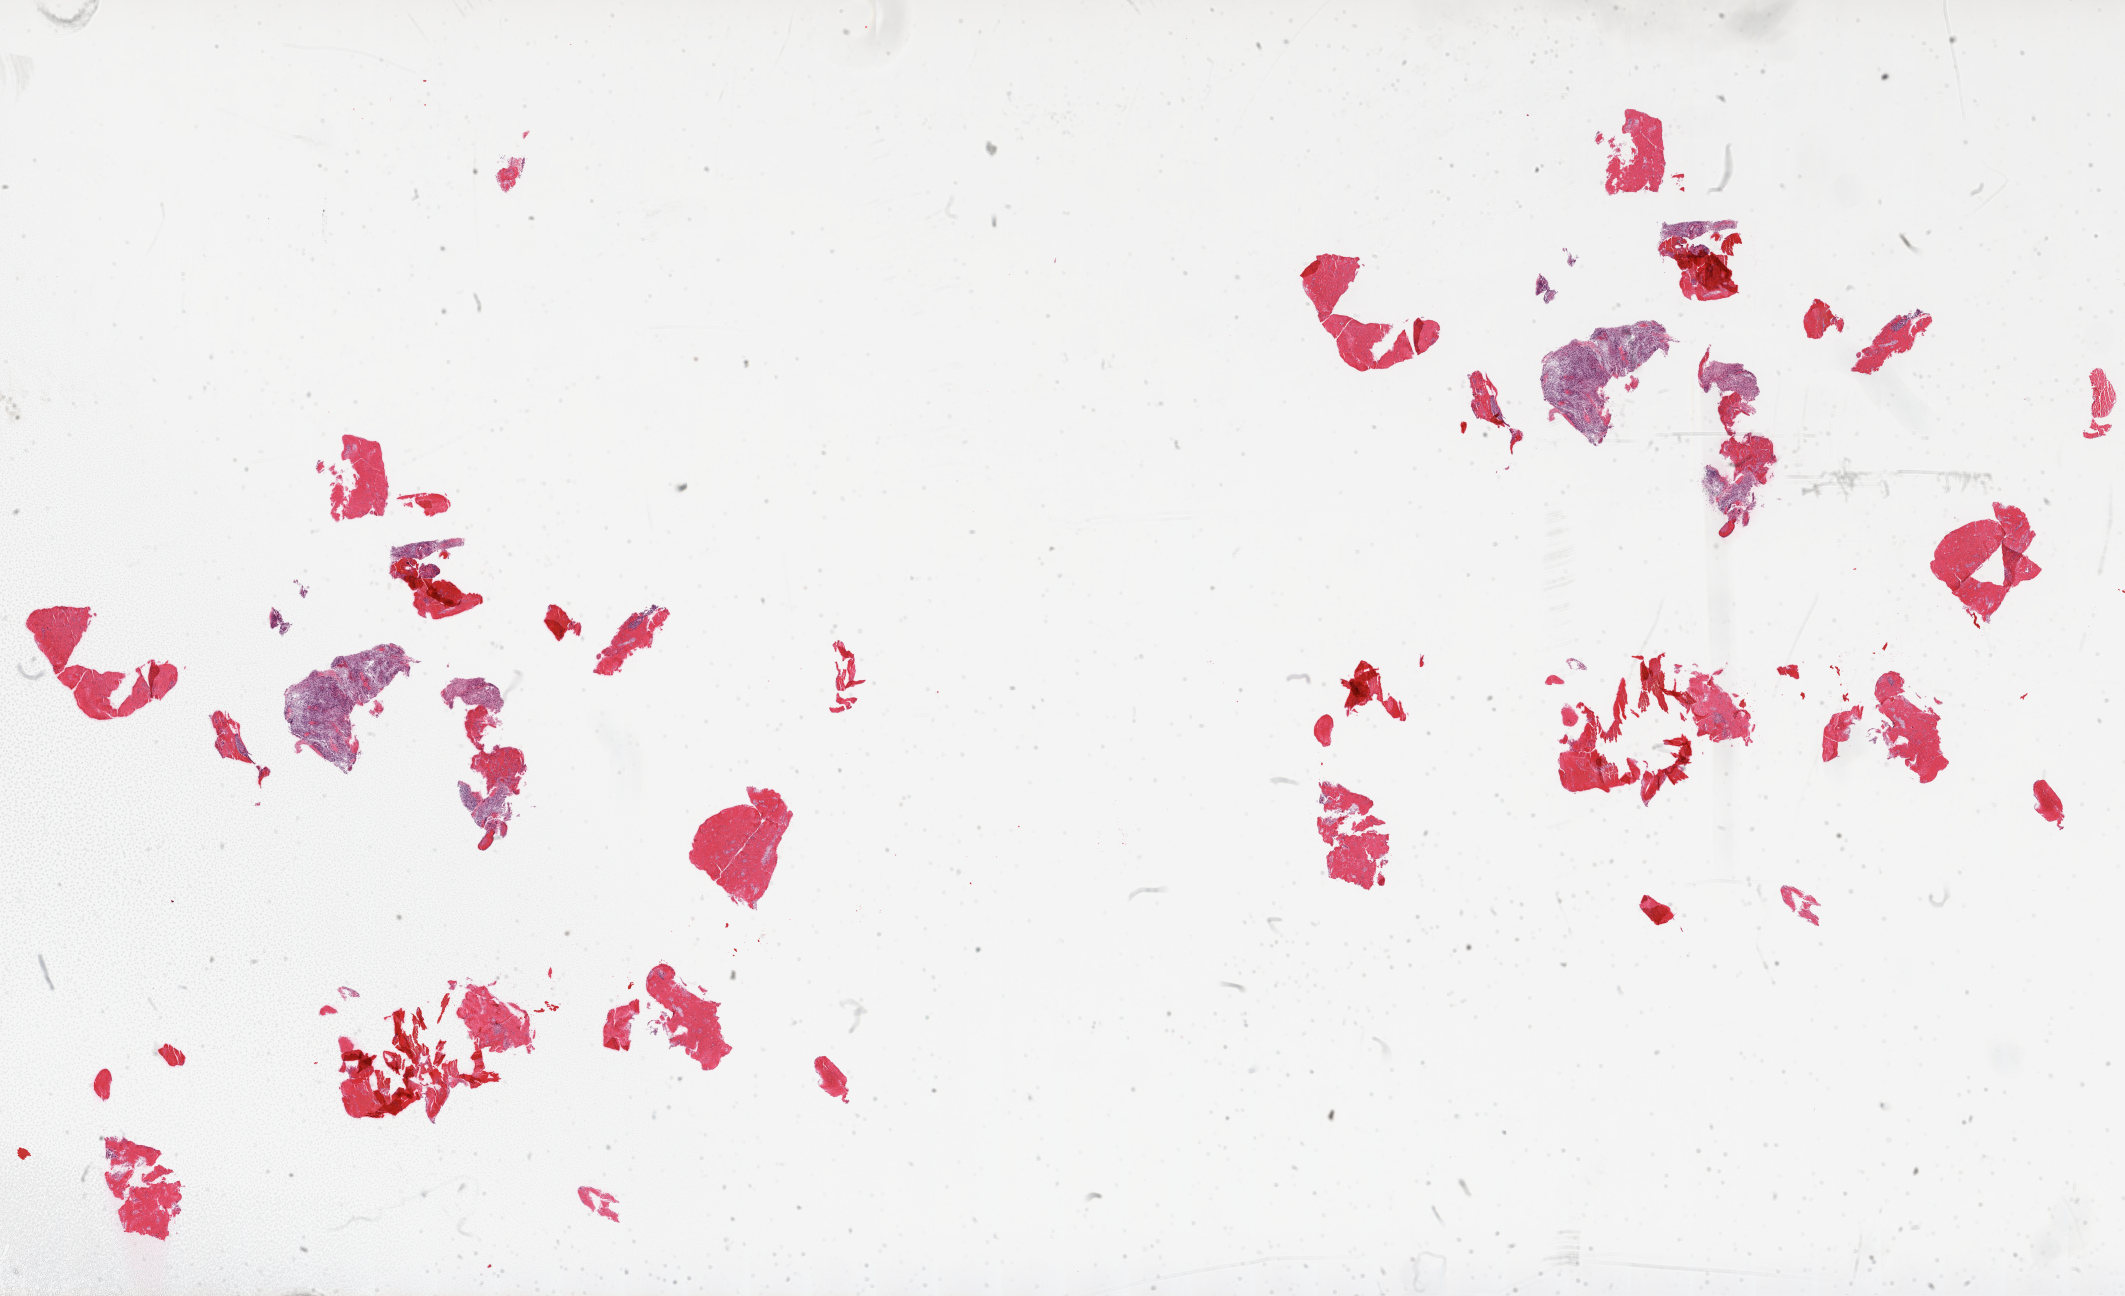
Hematoxylin and eosin (H&E) stained whole-slide image, whole scanned area (about 34.1 x 20.8 mm, slide scanned at 20x) shown as a low-resolution overview, FFPE section, brain, primary tumour sample. Male, age 61 years at initial diagnosis.
Pathologic diagnosis: Glioblastoma.